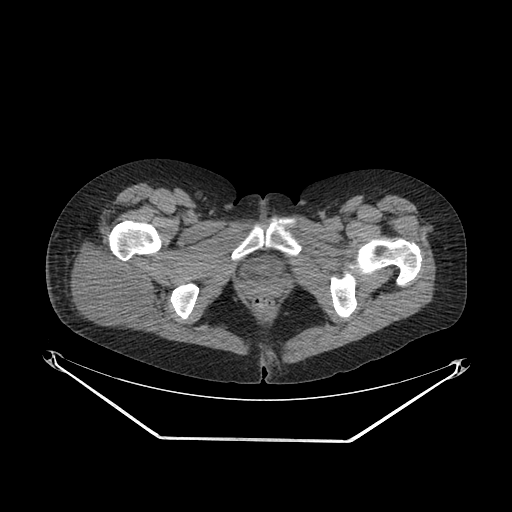
CT of an extremity soft-tissue mass (from a PET/CT study), one axial slice. Position 41 of 267 along the scan axis. 140 kVp. Soft-tissue window (W 400 / L 40 HU). 512 × 512 image matrix, field of view 500 × 500 mm. Female patient. From the clinical record (not read from this slice): histological type: epithelioid sarcoma with vascular differentiation; site of the primary tumour: right buttock.
Structures marked on this image (expert contour drawn on MRI and transferred to this co-registered scan by the dataset authors):
- gross tumour volume (mass): bounding box (x1, y1, x2, y2) in pixels: (66, 240, 156, 332)